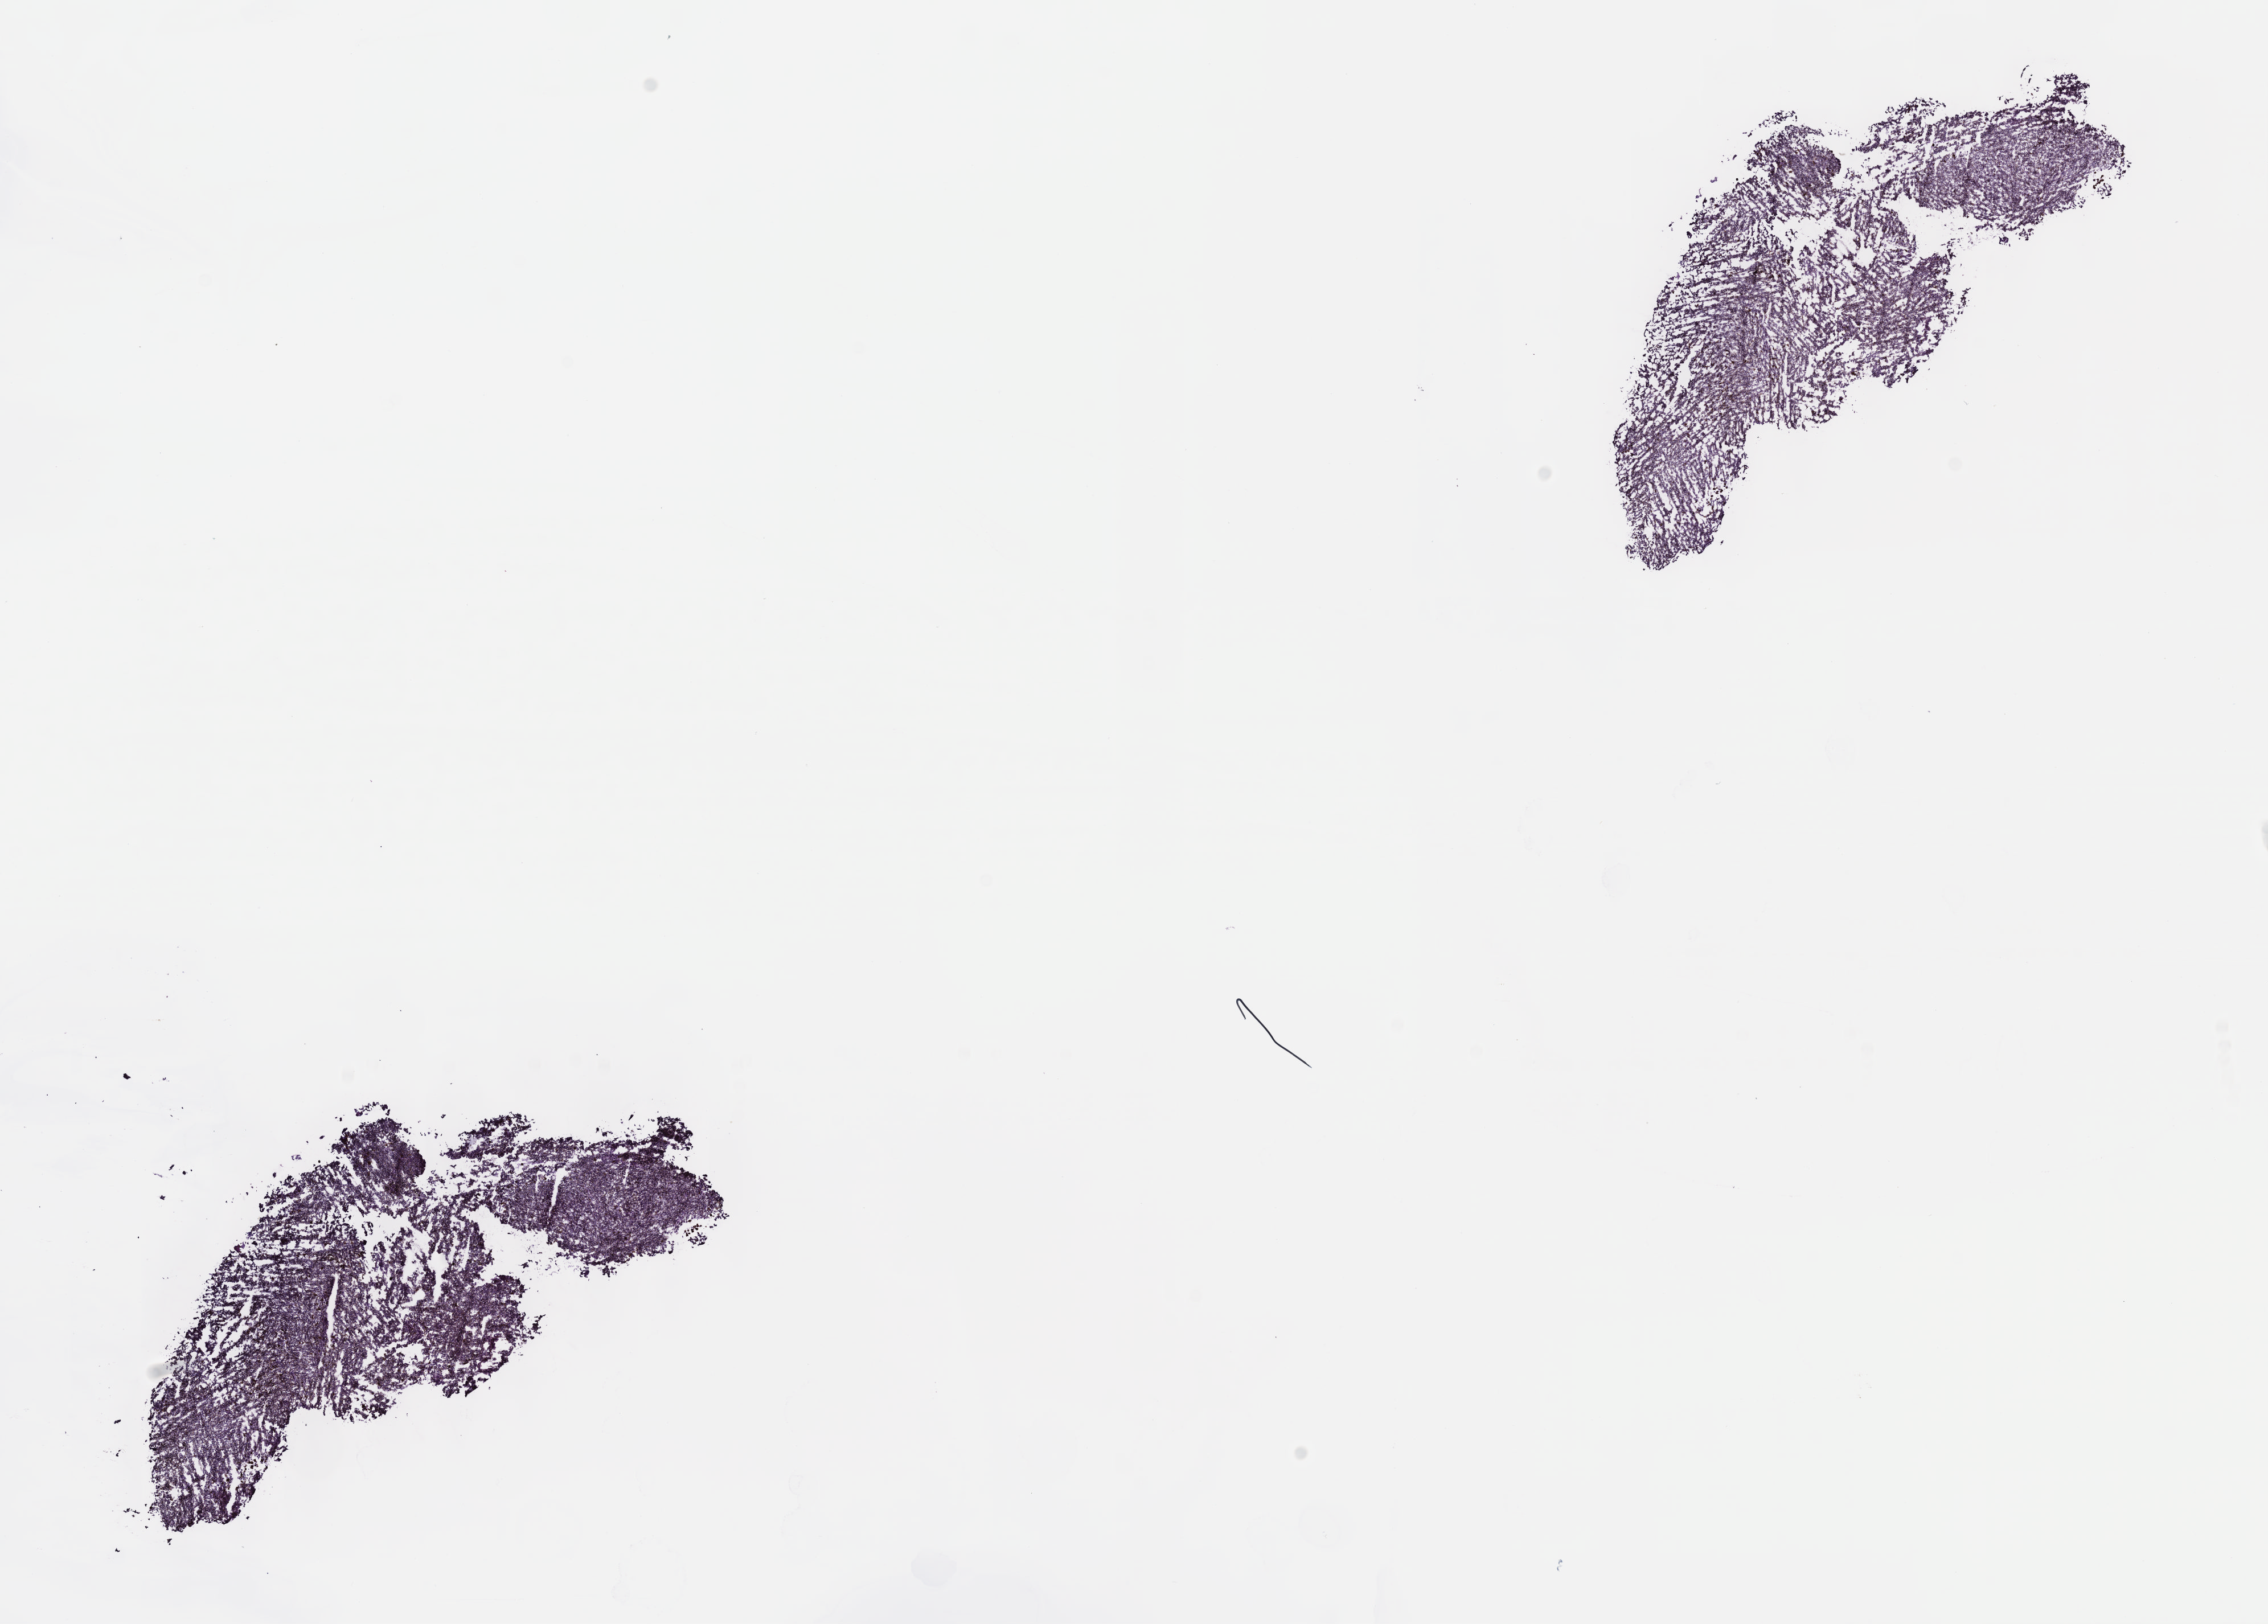
Whole-slide histology image, Hematoxylin and eosin (H&E) stained, shown as a low-resolution overview of the whole scanned area (about 16.1 x 11.5 mm), frozen section from the top of the tissue portion, uvea, primary tumour sample. Male, age 75 years at initial diagnosis. Pathologist review of this section (percent, as recorded): tumour cells 85%, tumour nuclei 85%, normal cells 0%, stromal cells 15%, necrosis 0%. Inflammatory infiltration, as recorded: lymphocyte infiltration 0%, monocyte infiltration 0%, neutrophil infiltration 0%.
- AJCC pathologic stage: IIB (7th edition)
- pathologic diagnosis: Spindle cell melanoma, NOS (choroid)